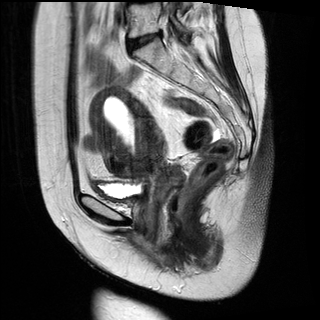
Pelvic MRI for cervical cancer, one sagittal slice; slice 15 of 28 in the series (ordered by position); T2-weighted; 1.5 T; TE 89 ms, TR 2740 ms; 320 × 320 image matrix. Patient: female, 49 years.
Annotated regions visible in this slice (expert manual segmentation):
- uterus and cervix: bounding box [x1, y1, x2, y2] px = [87, 87, 186, 206]